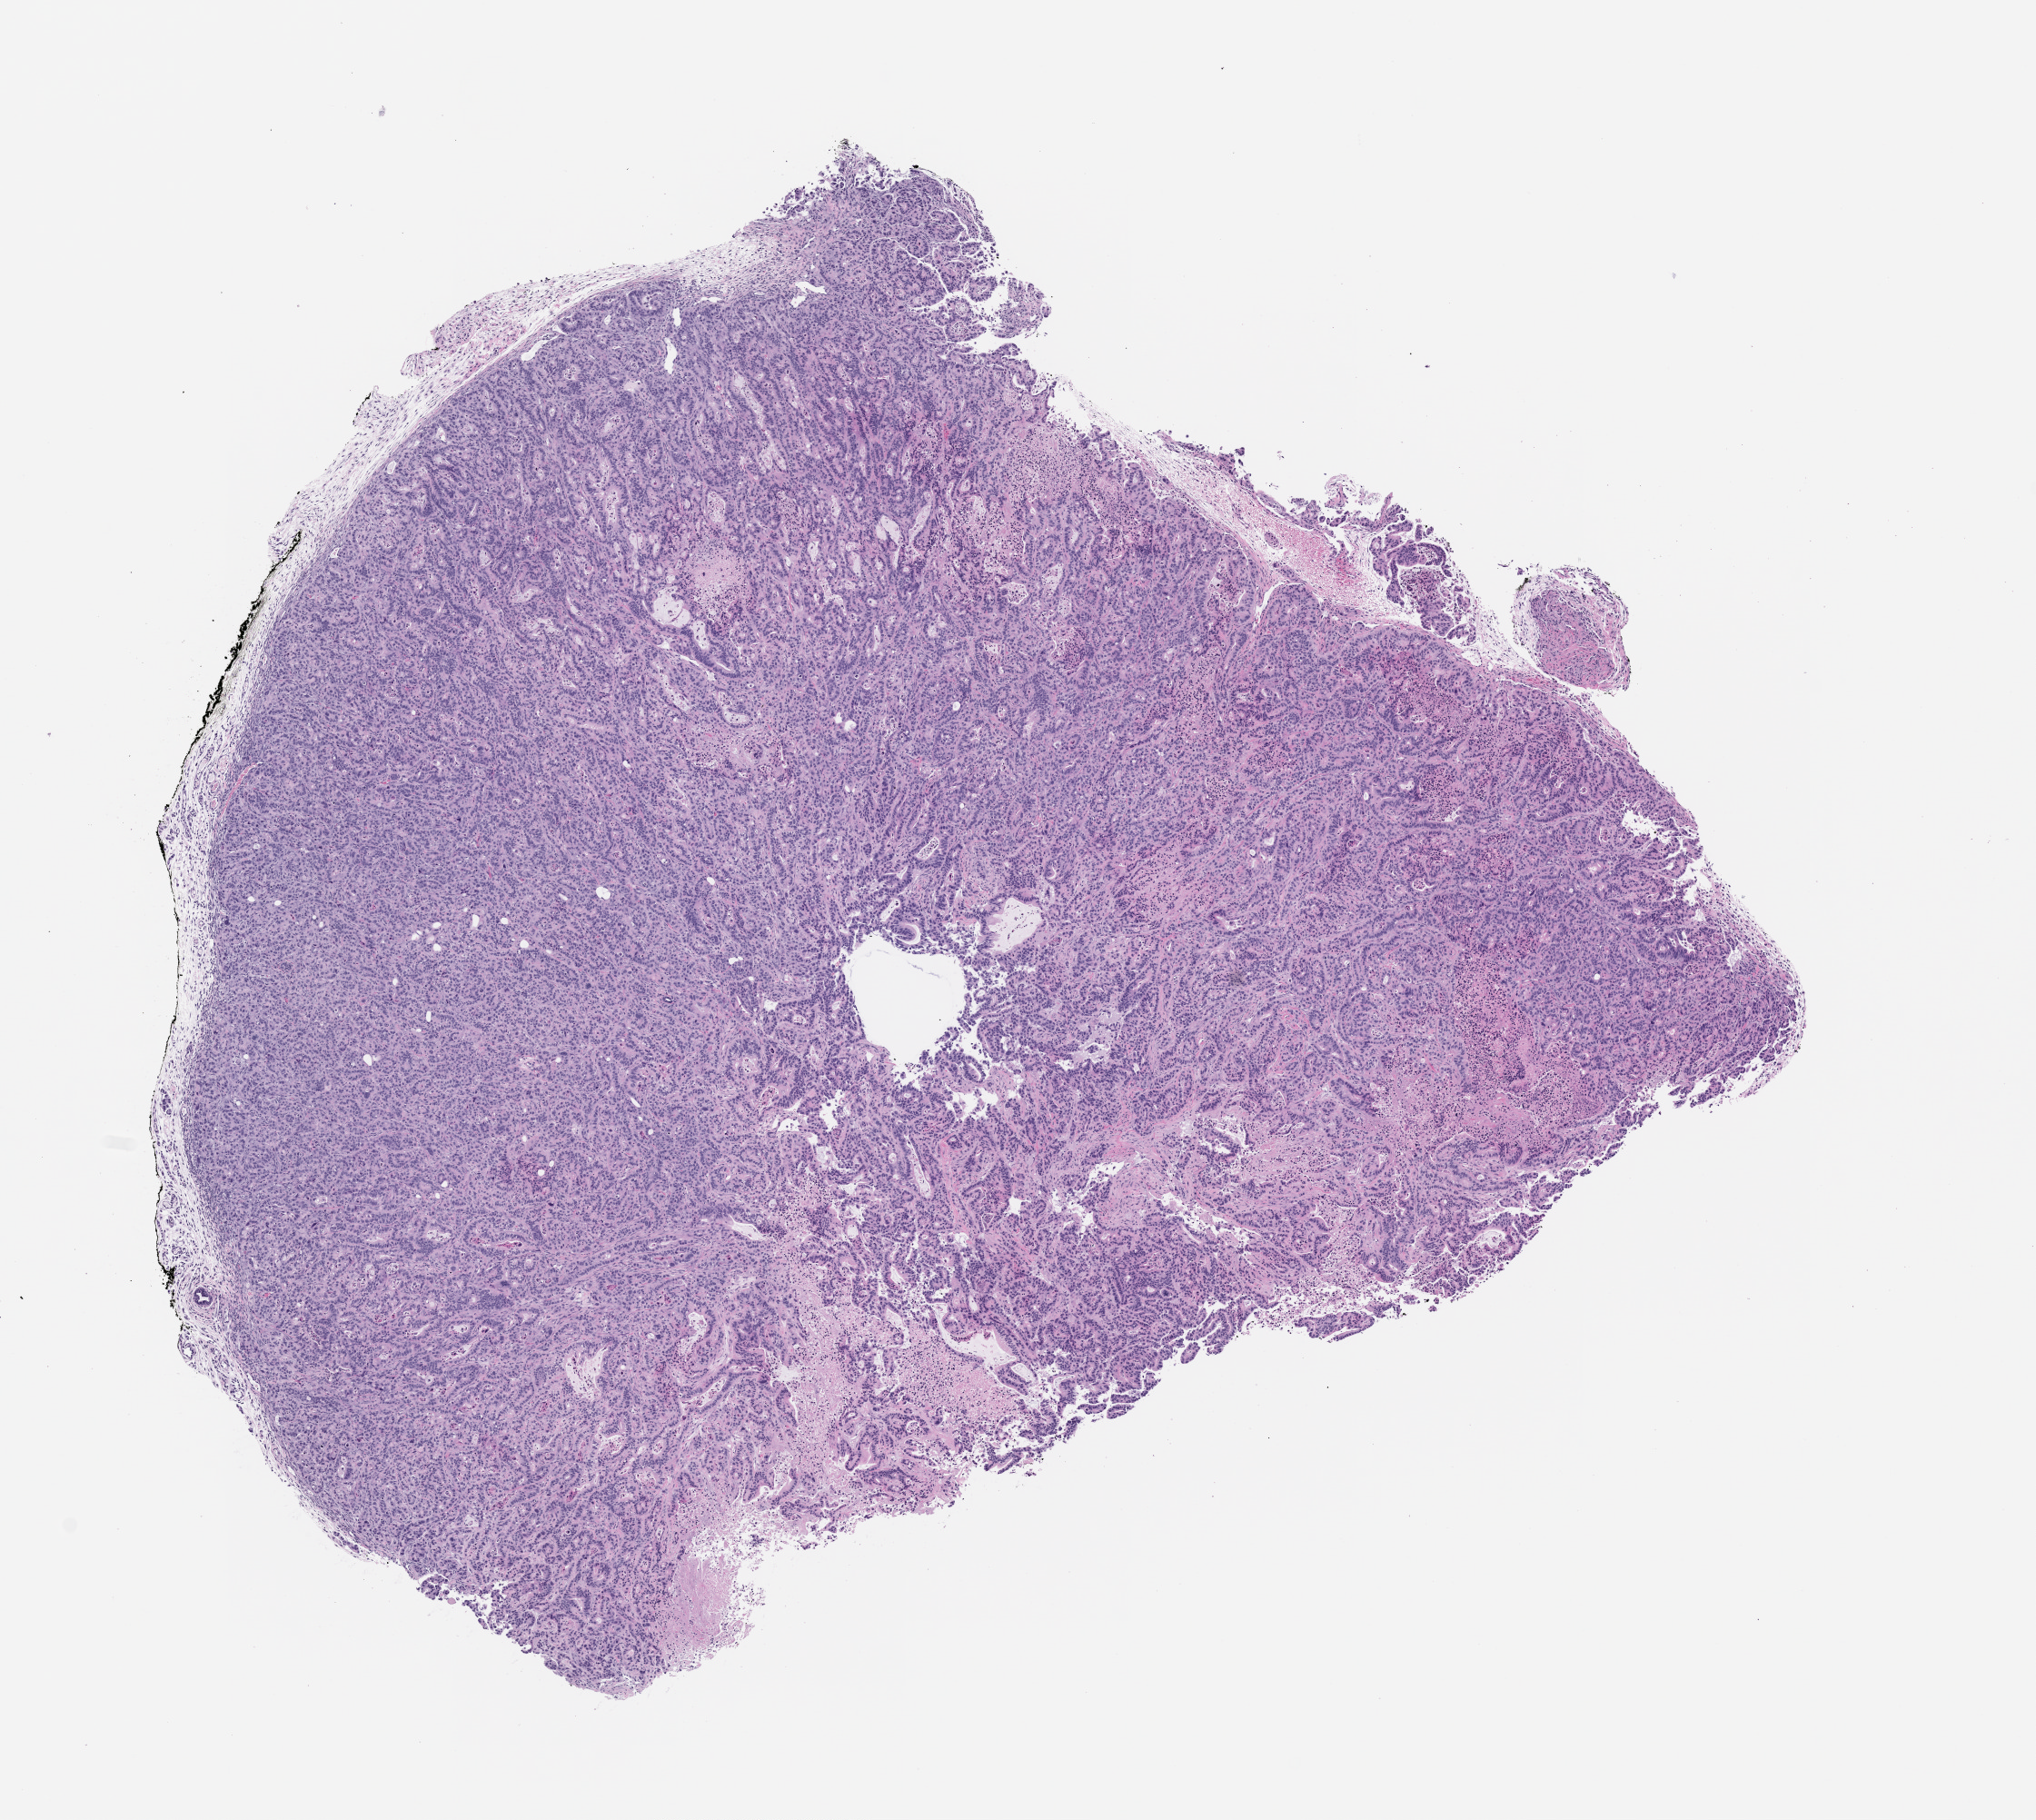
Hematoxylin and eosin (H&E) whole-slide image of a patient-derived xenograft (PDX) tumor grown in a mouse, passage 1 — whole scanned area (about 9.0 x 8.1 mm) shown as a low-resolution overview; formalin-fixed, paraffin-embedded (FFPE) tissue; originating tumor site category: pancreas.
Originating patient diagnosis: Pancreatic Adenocarcinoma.